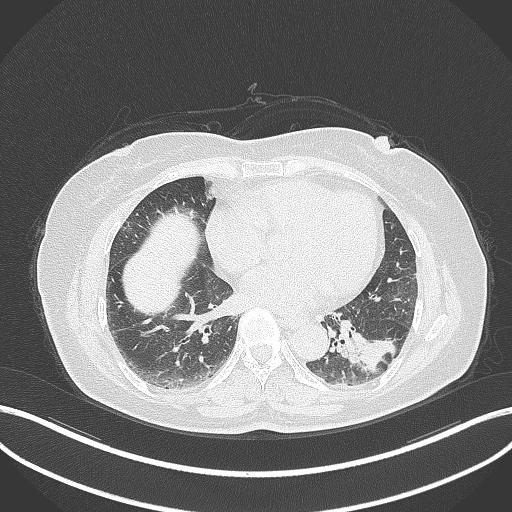
Chest CT, one axial slice; position 151 of 311 along the scan axis; 120 kVp; lung window (W 1500 / L -600 HU); 1 mm slice thickness; 512 × 512 image matrix. Patient: female, 59 years. Case-level facts recorded for this patient, not image findings: clinical TNM (as recorded): T2a N0 M0.
Annotated regions visible in this slice (rectangle marked by the reading radiologist):
- lung tumour (recorded histology: adenocarcinoma): bounding box [x1, y1, x2, y2] px = [344, 321, 398, 377]